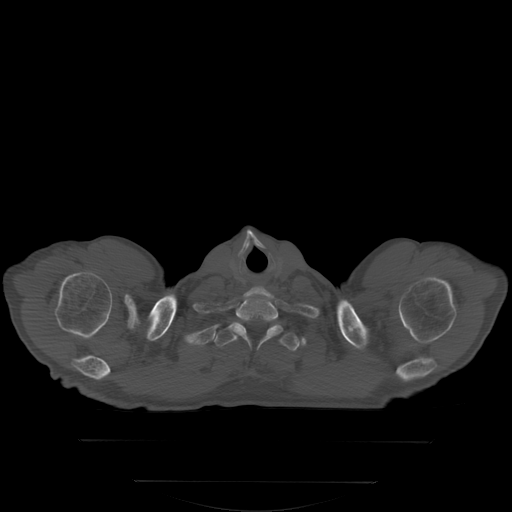
CT including the spine, one axial slice. Slice 293 of 350 in the series (ordered by position). Bone window (W 1800 / L 400 HU). 512 × 512 image matrix, field of view 500 × 500 mm. Patient: male, 58 years. From the clinical record (not read from this slice): primary cancer: prostate; vertebrae with lytic lesions (as recorded): L1.
Structures marked on this image (semi-automatically segmented with operator editing):
- T1 vertebra: bounding box [x1, y1, x2, y2] px = [222, 323, 300, 350]